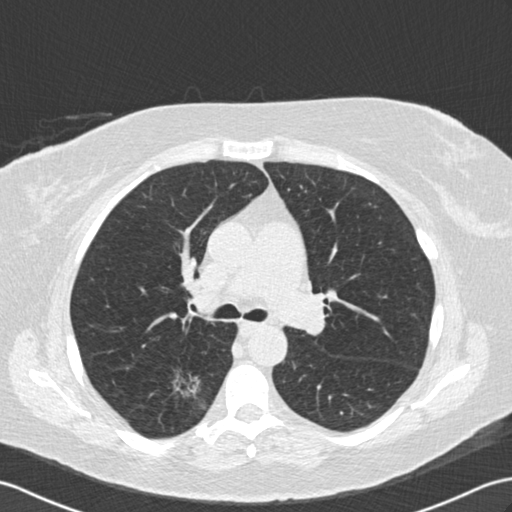
Axial slice from a low-dose chest CT screening exam. Second screening round (one year after baseline). Lung window (W 1500 / L -600 HU). 2 mm slice thickness. 120 kVp. Slice 56 of 154 in the series. Female participant, aged 65 years at enrolment. Former smoker at enrolment.
Lesion marked by an expert reader, box from (x=157, y=357) to (x=216, y=415) px. The exam's reader record, not a measurement of the box and not confirmed to be the same lesion: non-calcified nodule or mass ≥4 mm, right lower lobe, 18 × 16 mm, spiculated (stellate) margins, soft tissue attenuation, pre-existing on the prior screen: yes; interval growth: yes.